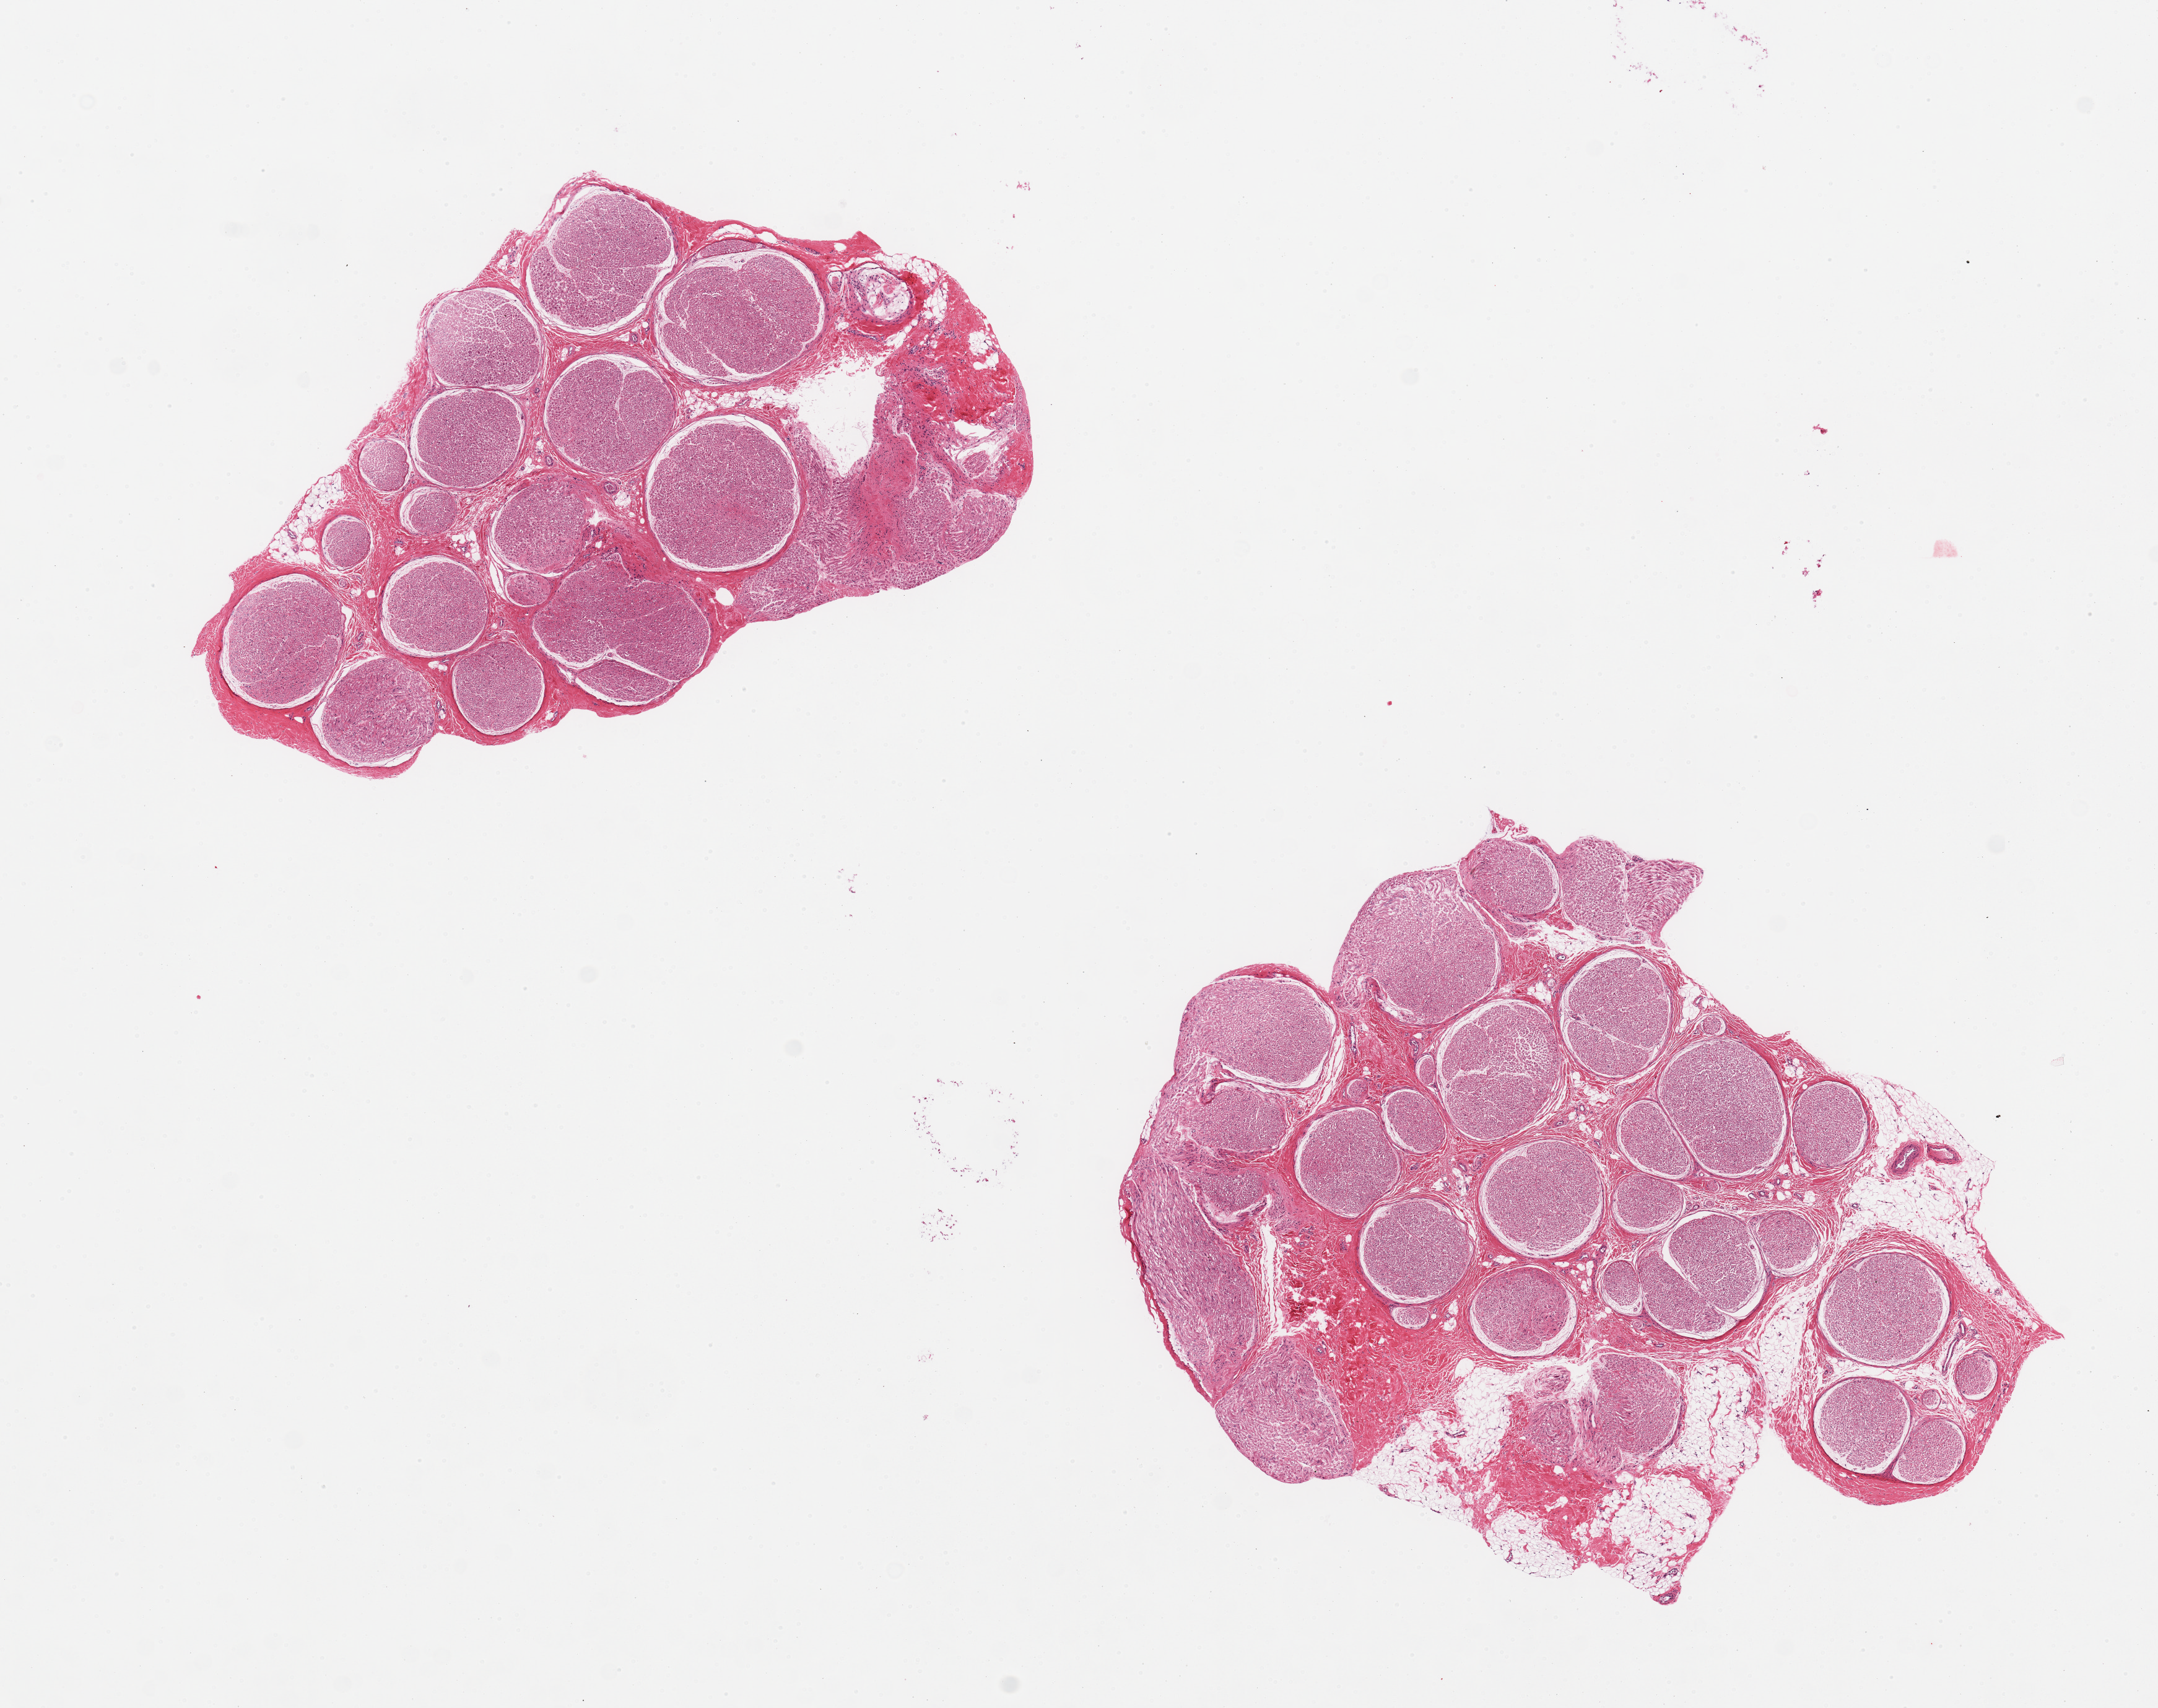
Whole-slide image, hematoxylin and eosin (H&E) stain — low-resolution overview of the scanned area, about 13.8 x 10.9 mm (acquisition: 20x scan), PAXgene-fixed, paraffin-embedded tissue, section of tibial nerve (target tissue), donor tissue sample. Donor: female.
Review note (as recorded): 2 pieces, one ~10% fat.